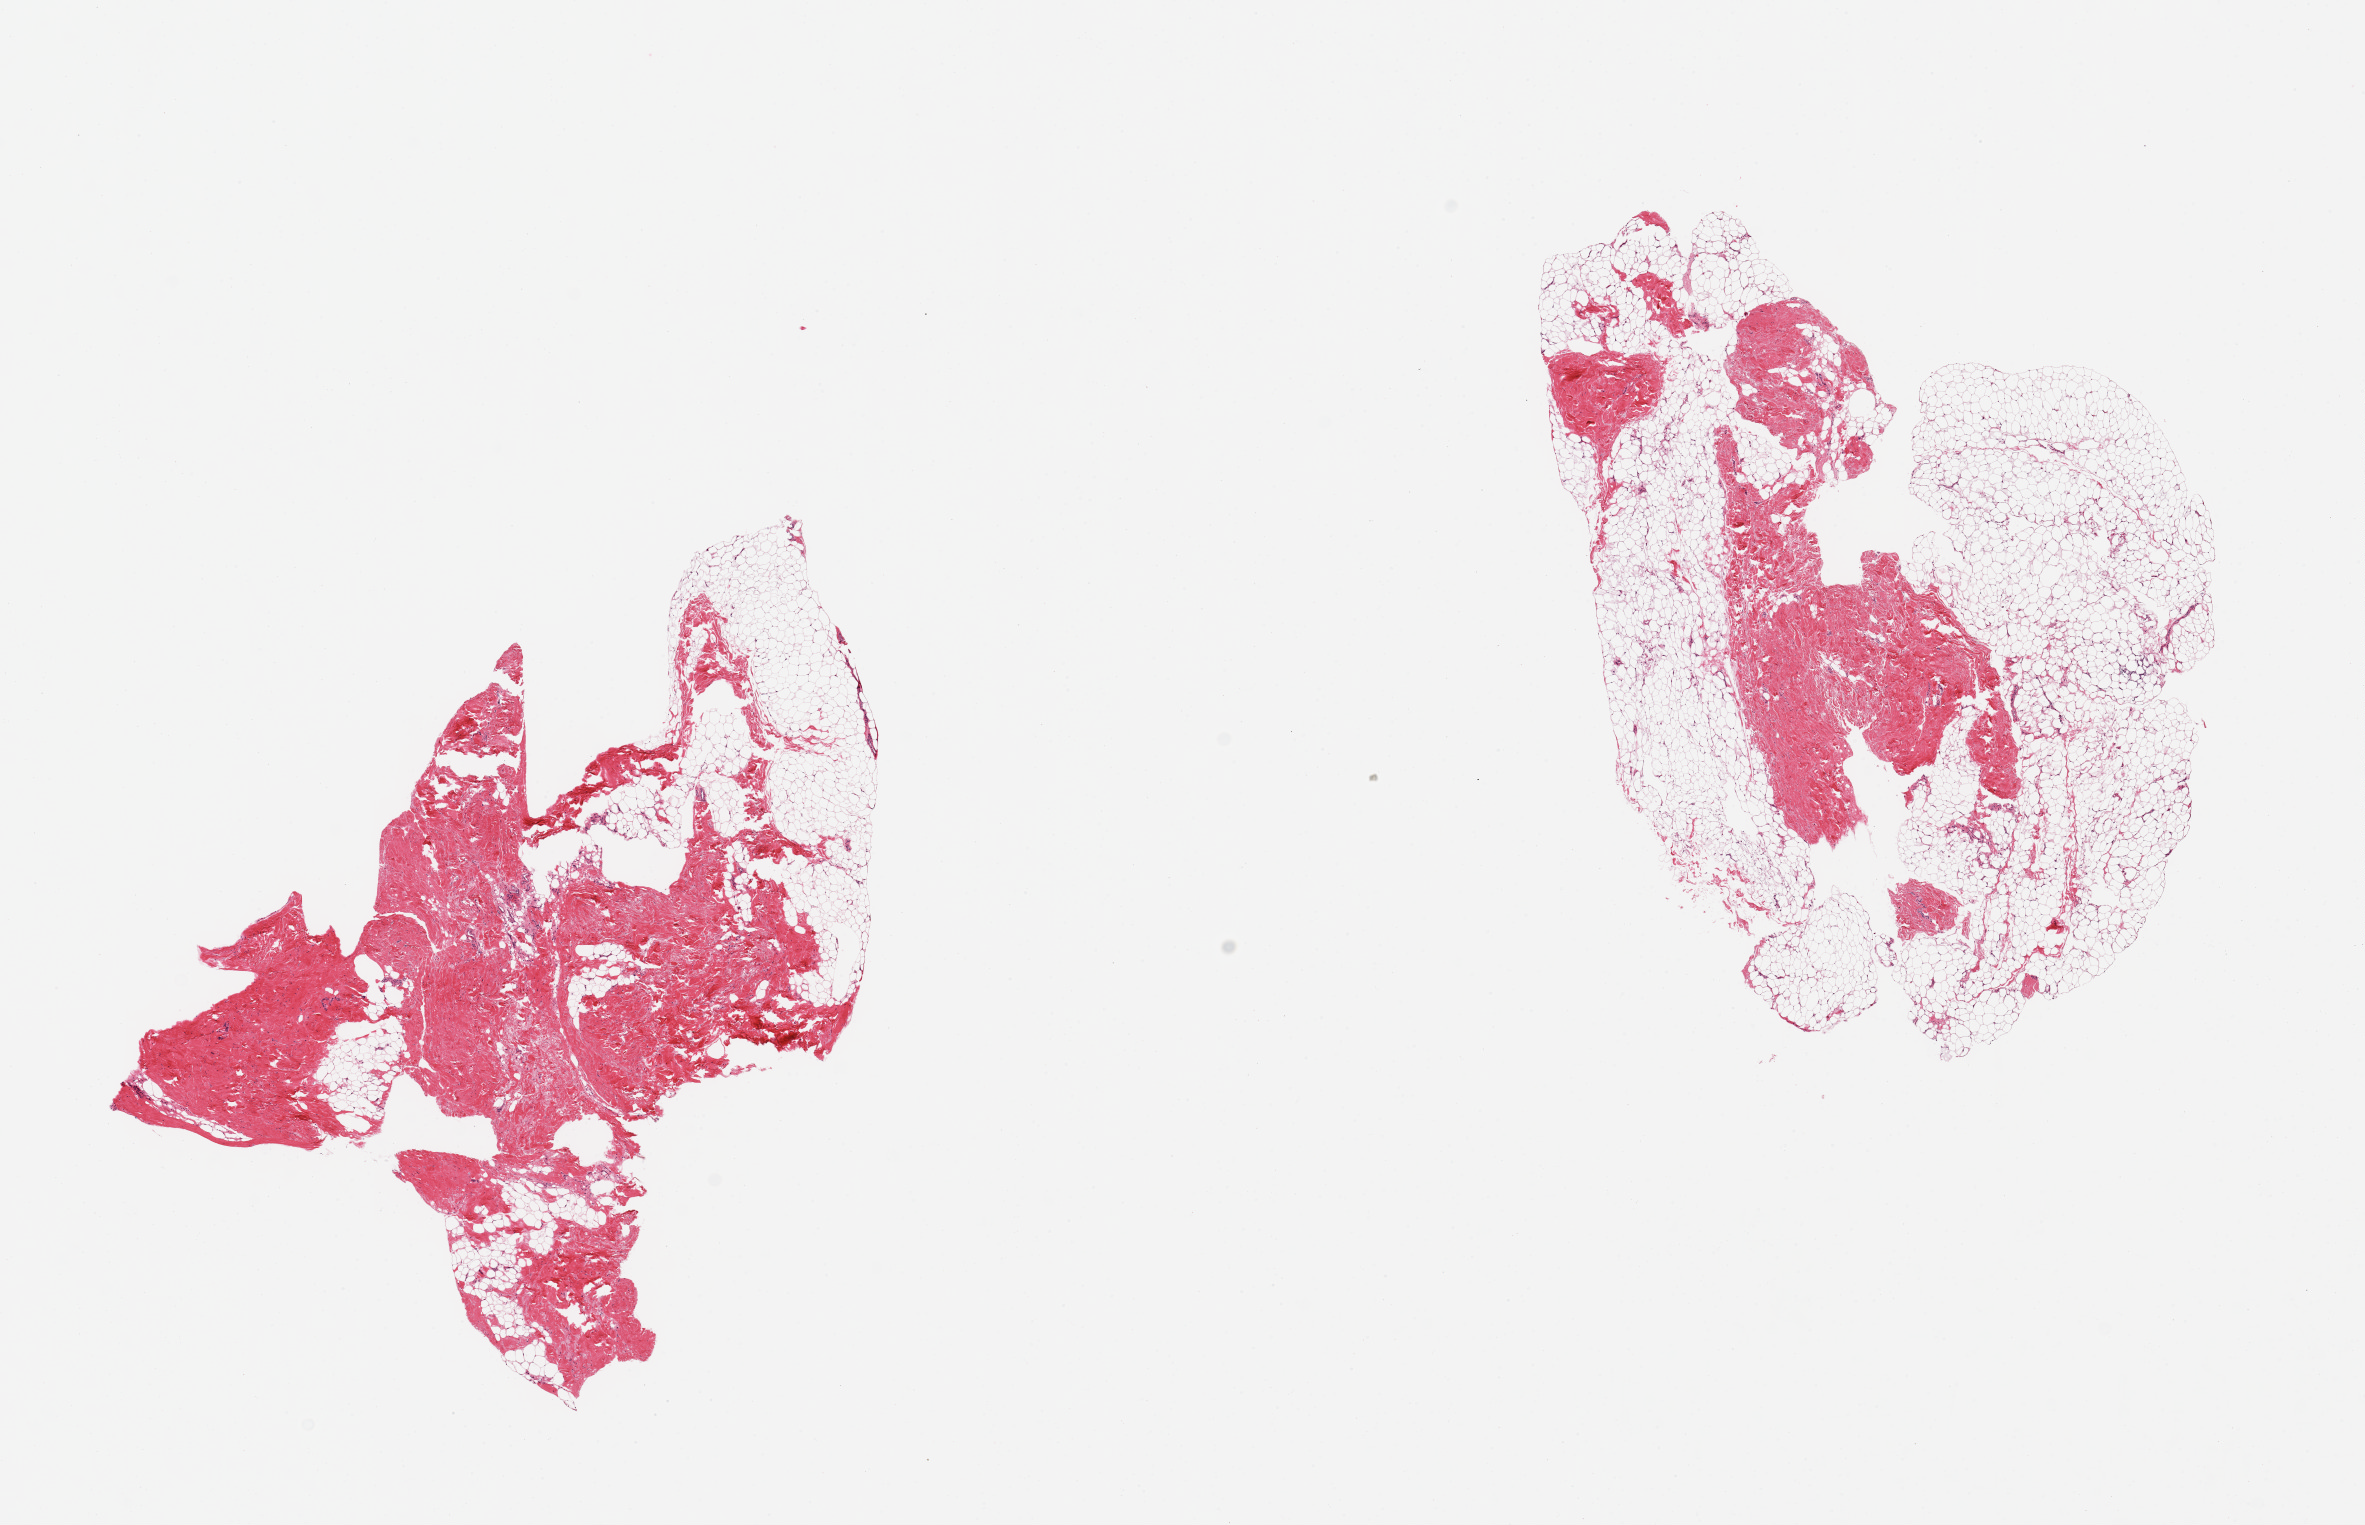
Digitized hematoxylin and eosin (H&E)-stained section, brightfield — shown as a low-resolution overview of the whole scanned area (about 18.7 x 12.1 mm). PAXgene-fixed, paraffin-embedded tissue. Section of breast (target tissue). Tissue donor sample.
- reviewer comment on this tissue sample: 2 pieces, fibroadipose tissue only, no ductal elements